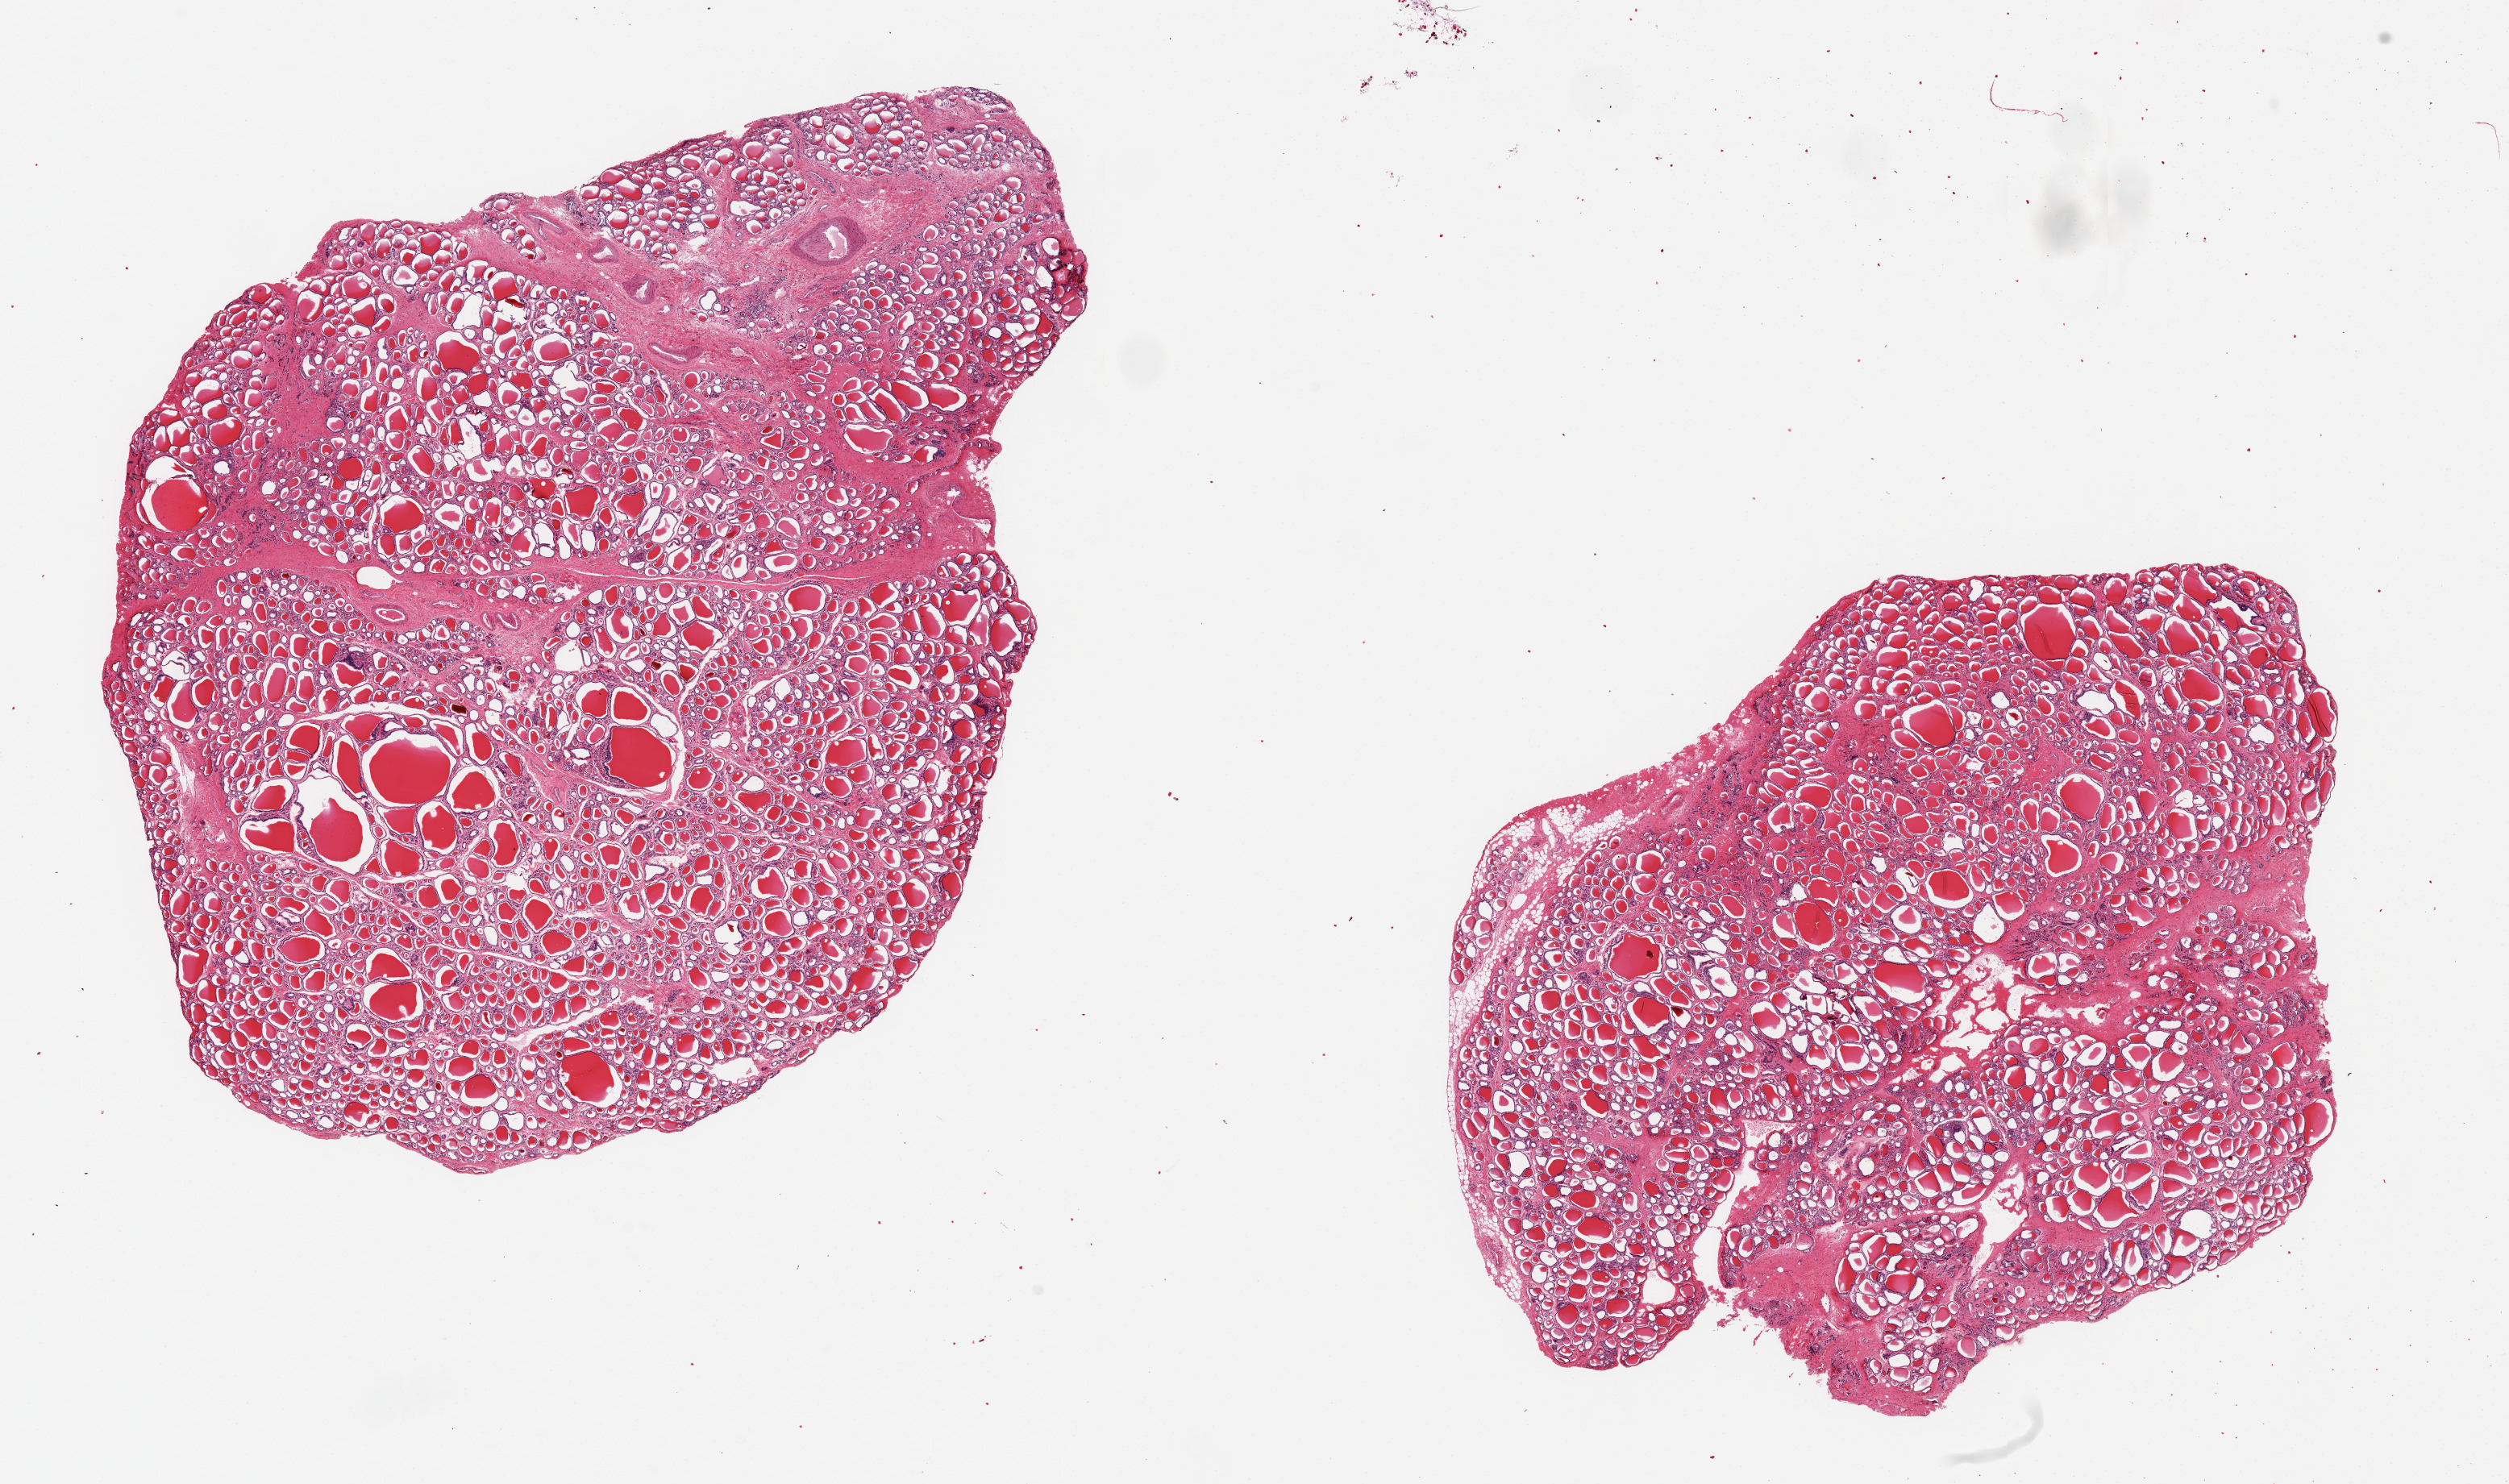
Digitized haematoxylin and eosin-stained section, brightfield — low-resolution overview of the scanned area, about 24.6 x 14.6 mm (from a 20x scan); PAXgene-fixed paraffin-embedded (PFPE) section; section of thyroid (target tissue); donor tissue sample. Male donor.
* reviewer comment on this tissue sample: 2 pieces ~11x8mm, focal regressive areas